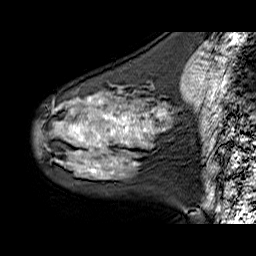
Breast MRI (dynamic contrast-enhanced), one sagittal slice; position 20 of 60 along the scan axis; dynamic contrast-enhanced series, time point 2 of 6 at this slice position (early post-contrast); 1.5 T; TE 6.3 ms, TR 32.9 ms; 4 mm slice thickness; 256 × 256 image matrix, field of view 200 × 200 mm. Female patient. Case-level facts recorded for this patient, not image findings: setting: breast cancer imaged before/during neoadjuvant chemotherapy; receptor status: HER2-positive.
Structures marked on this image (semi-automatic segmentation, software-assisted and operator-edited):
- analysis volume of interest (the breast-tissue region the enhancement analysis was run in; not a lesion): bounding box (x1, y1, x2, y2) in pixels: (35, 84, 173, 180)
- tumour enhancement mask (voxels above the 100 % enhancement threshold inside the analysis volume of interest): (73, 99, 164, 173)